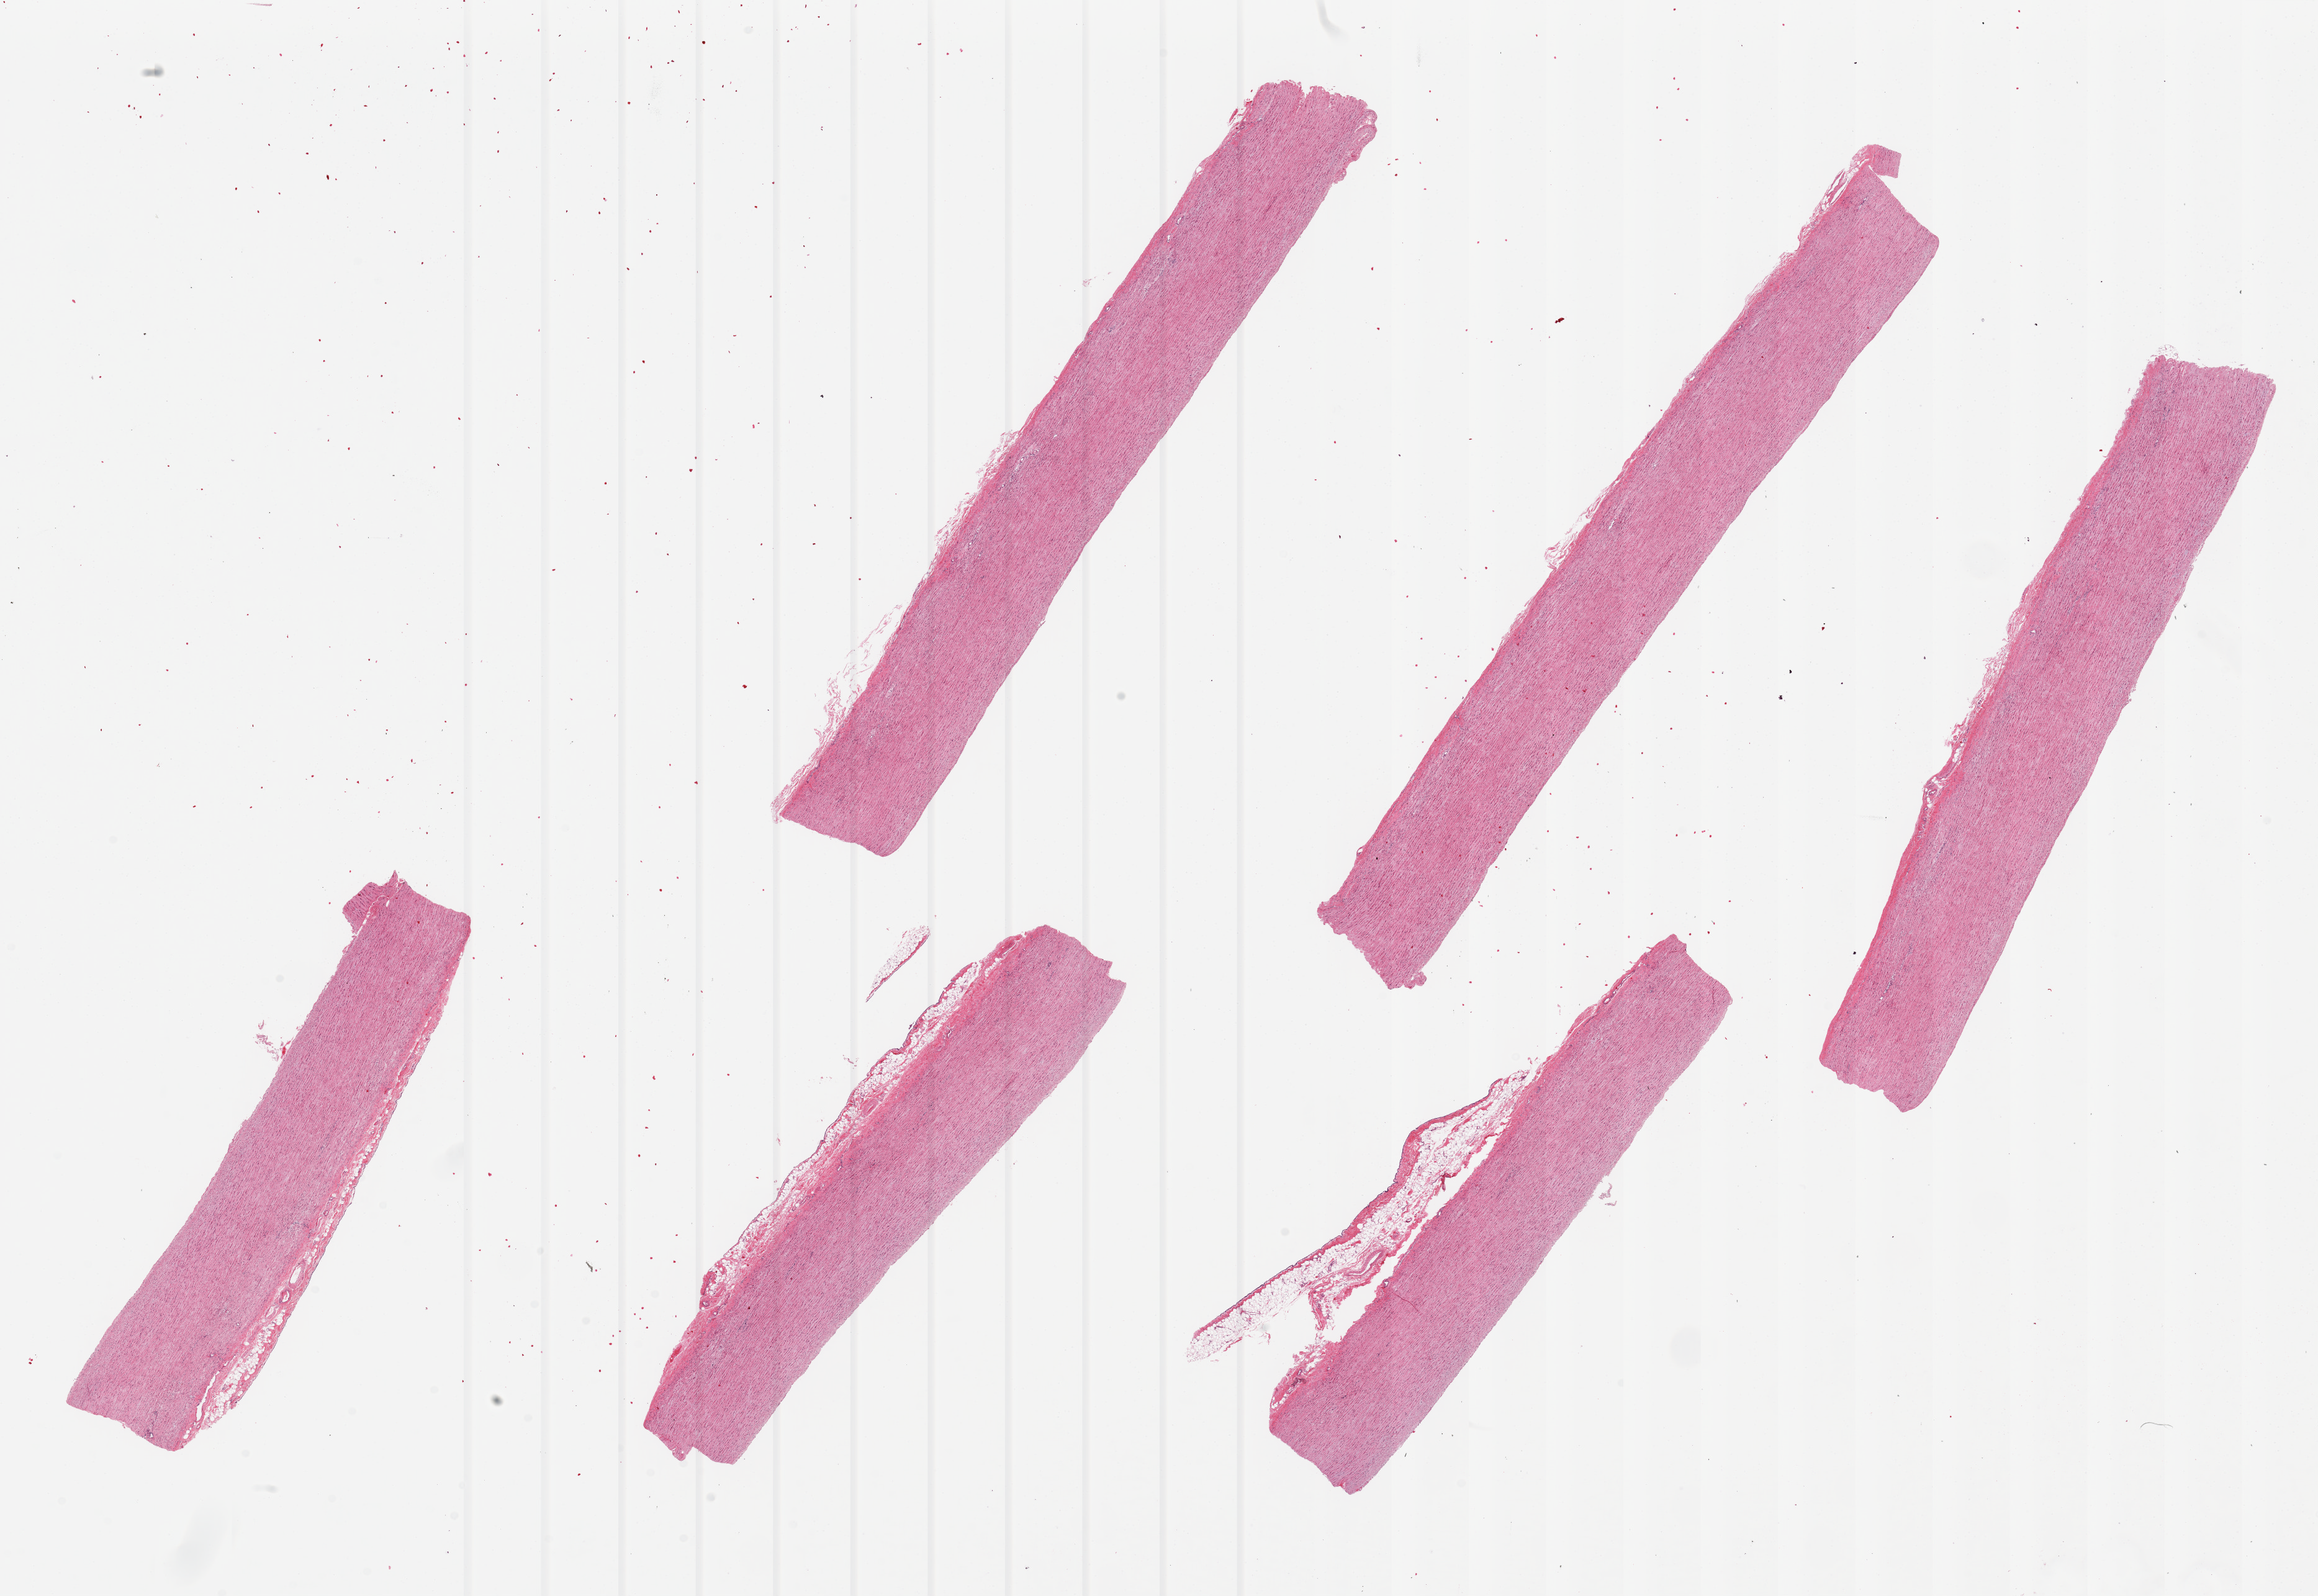
Hematoxylin and eosin (H&E) whole-slide image — whole scanned area (about 29.5 x 20.3 mm) shown as a low-resolution overview; PAXgene-fixed, paraffin-embedded tissue; section of aorta (target tissue); tissue donor sample. Male donor.
Pathologist's review note for this sample: 6 pieces ~11x2mm, minimal atherosis.